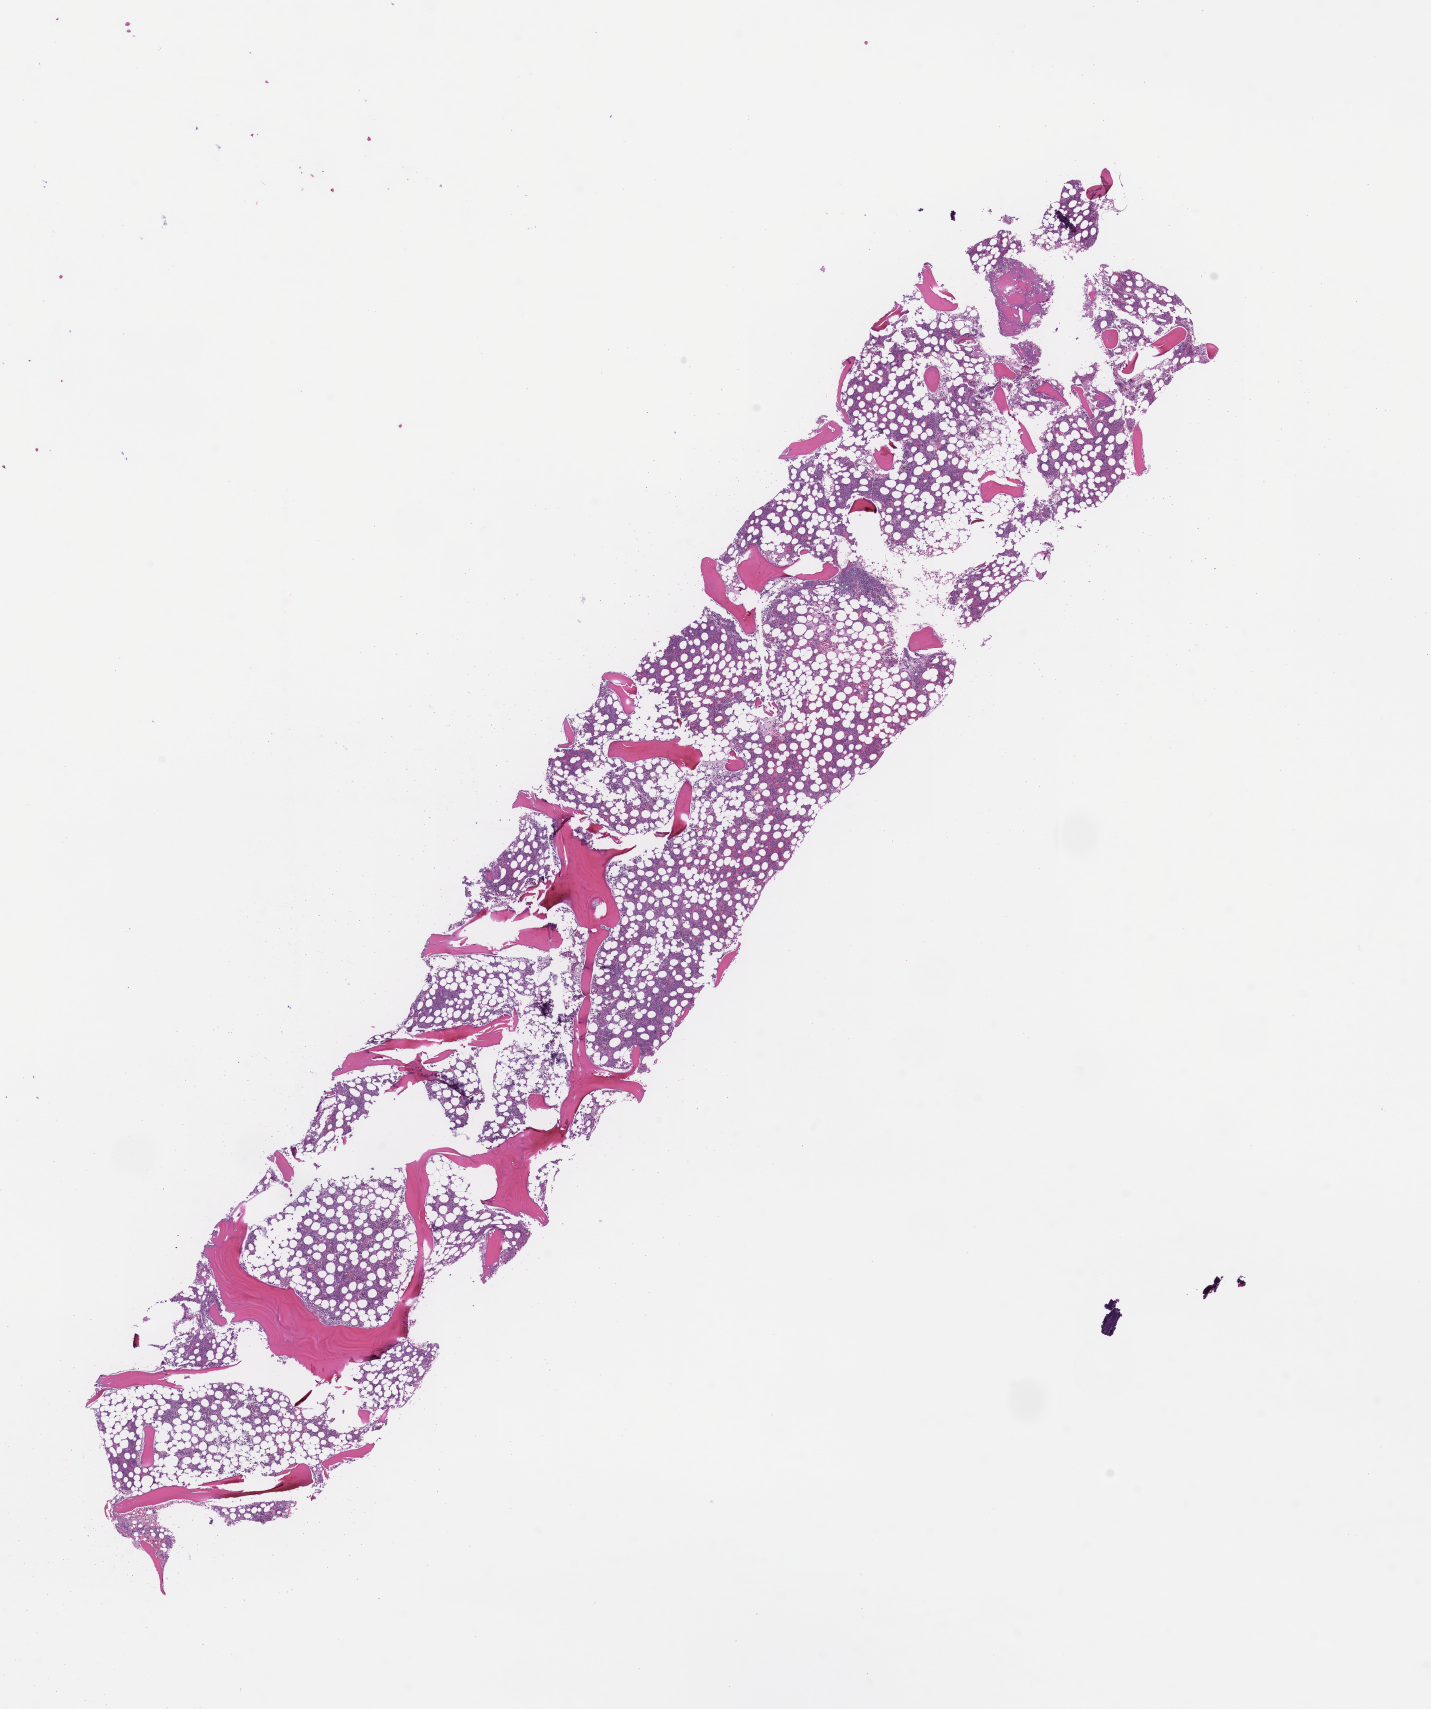
Whole-slide image, hematoxylin and eosin (H&E) stain, a low-resolution overview of the entire scanned area, about 11.6 x 13.8 mm, formalin-fixed, paraffin-embedded (FFPE) tissue, tissue site: bone marrow. Patient: male.
This section: primary tumor. Diagnosis: Plasma Cell Myeloma.